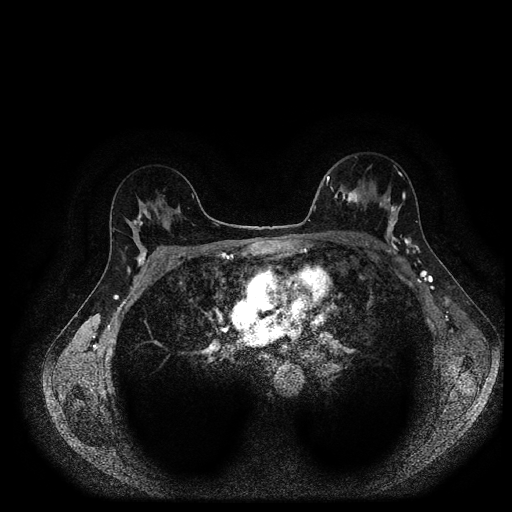
Breast MRI (dynamic contrast-enhanced, multi-phase), one axial slice. Position 66 of 116 along the scan axis. Dynamic contrast-enhanced series, time point 2 of 5 at this slice position (early post-contrast). 1.5 T. TE 2.7 ms, TR 5.4 ms. 2 mm slice thickness. 512 × 512 image matrix, field of view 340 × 340 mm. Female patient, age 40 years.
Structures marked on this image (semi-automatic segmentation, software-assisted and operator-edited):
- breast lesion (labelled 'tumour' in the annotation; benign lesions carry a separate 'benign' label): bounding box [x1, y1, x2, y2] px = [335, 187, 364, 205]